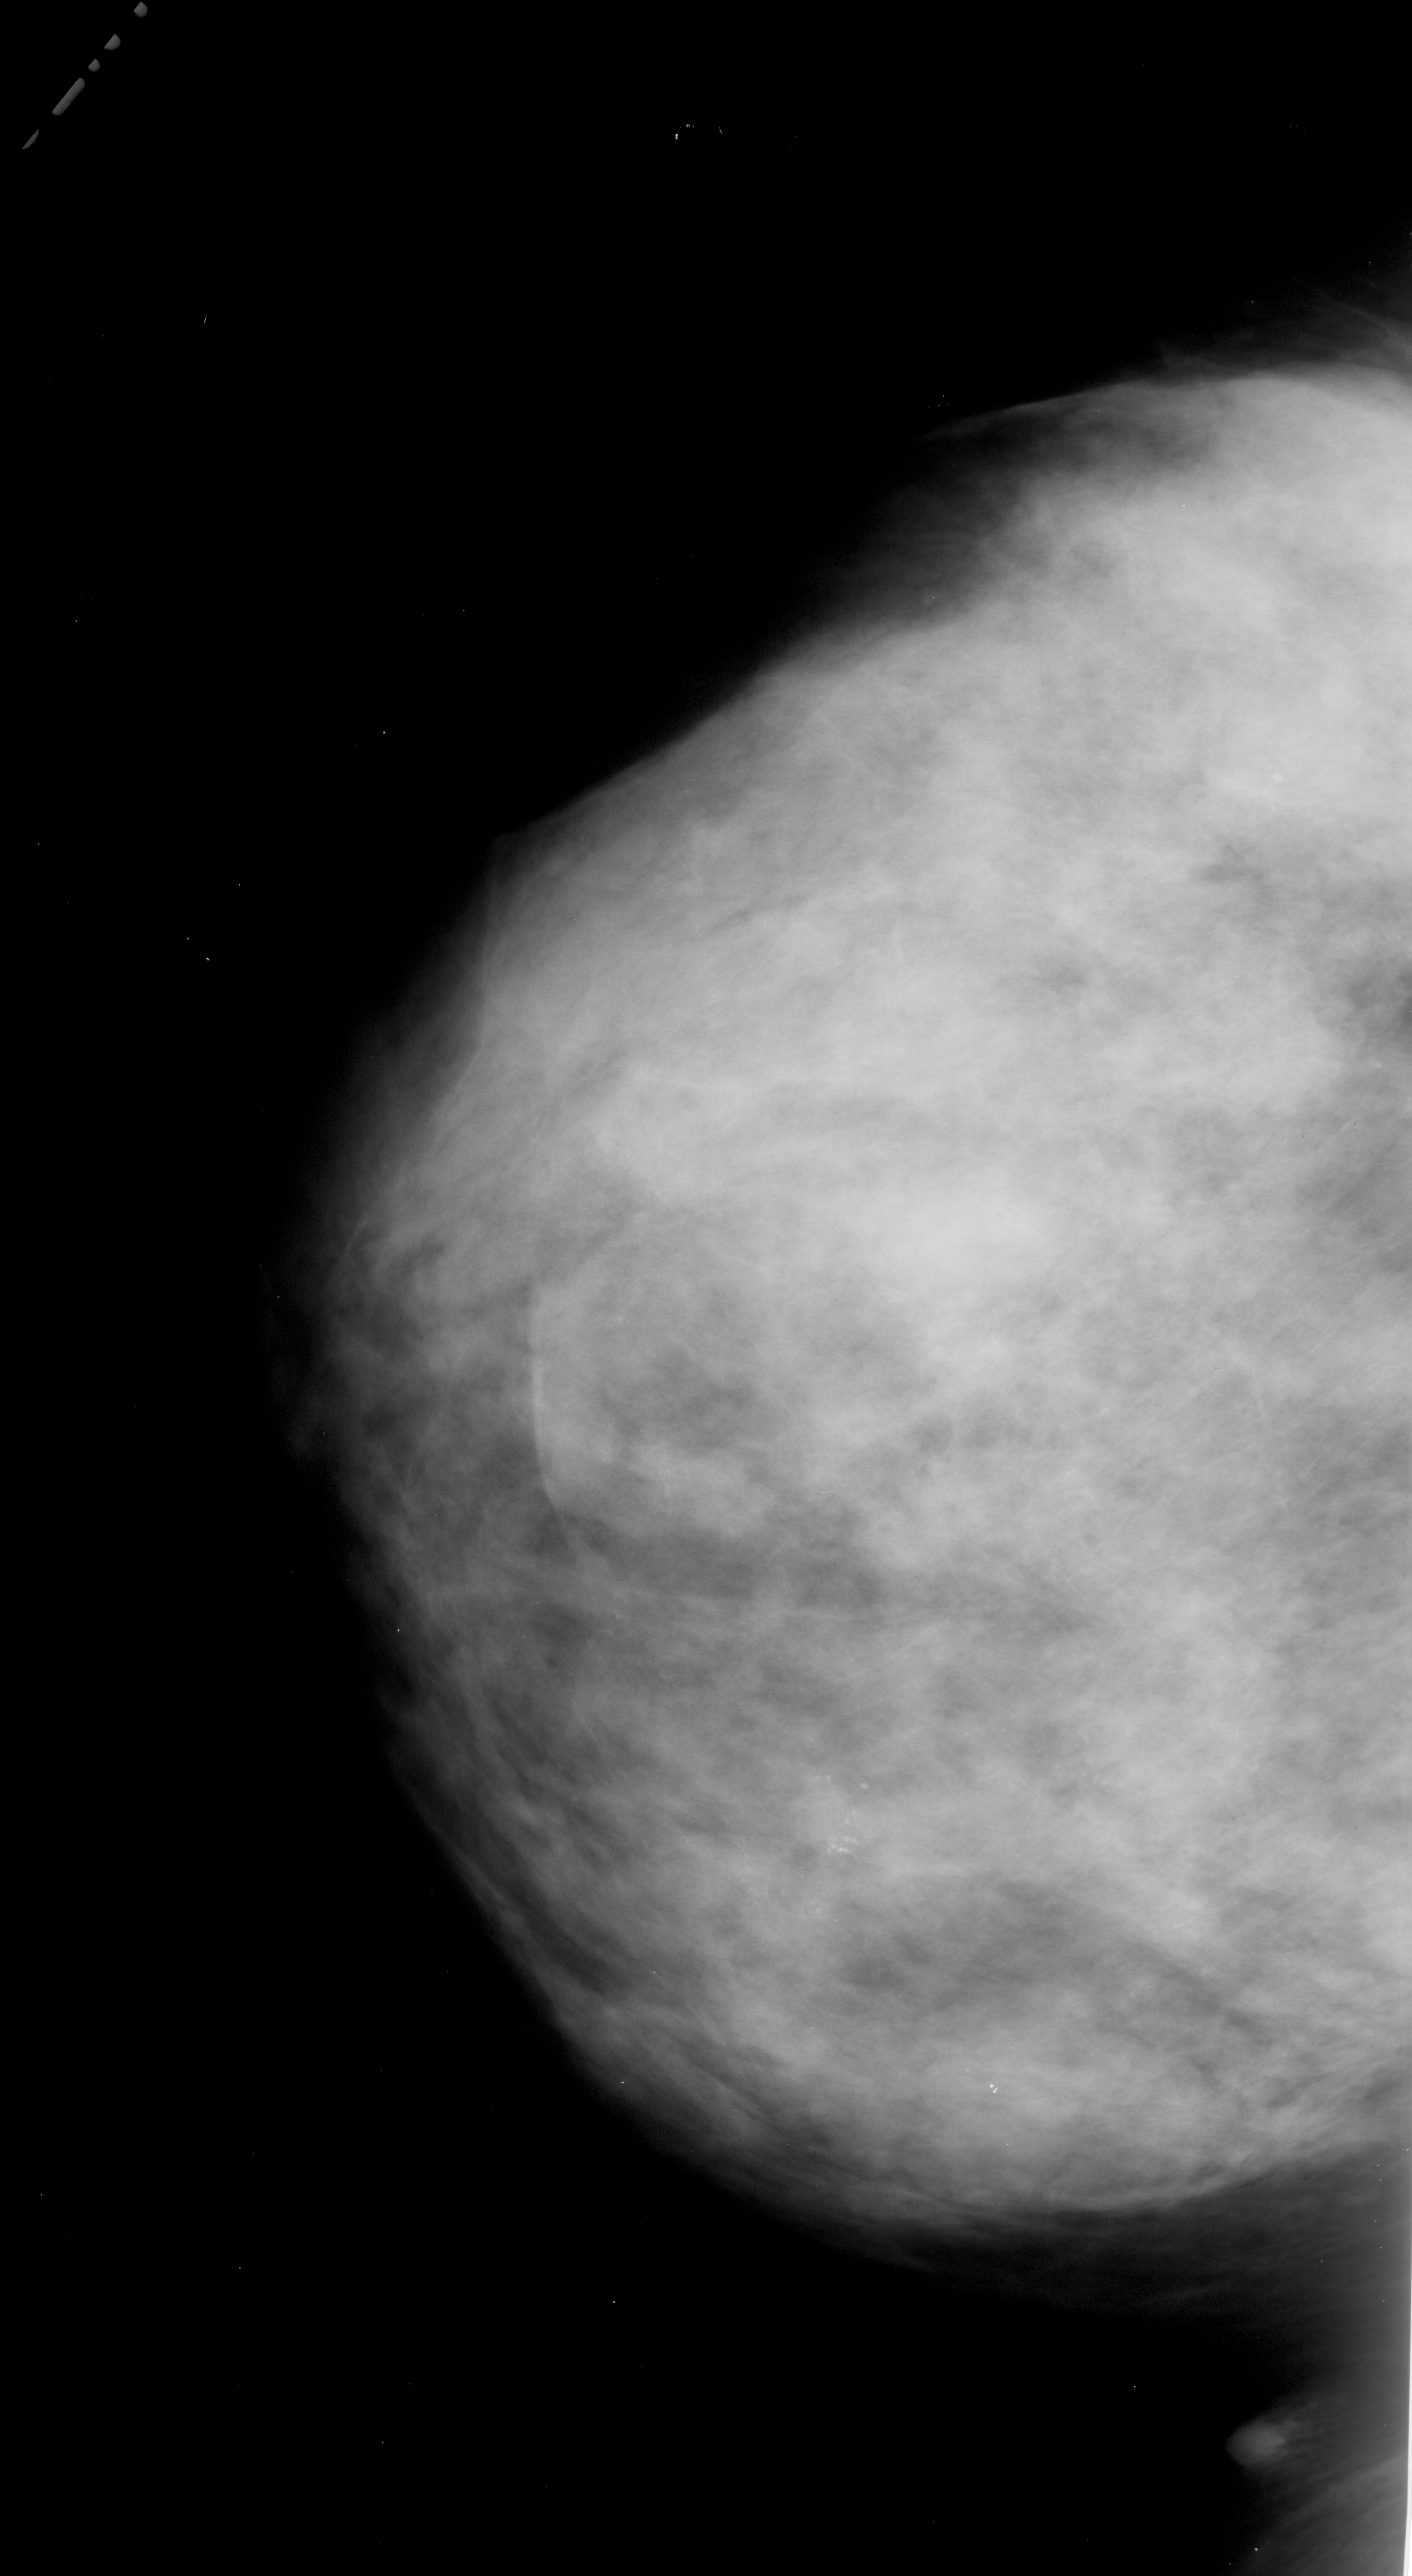
Scanned film-screen mammogram, left breast, craniocaudal (CC) view, breast composition: extremely dense (BI-RADS density category 4 of 4).
Marked abnormality: calcifications, morphology pleomorphic, distribution clustered; BI-RADS assessment category 4; pathology result (as recorded, not read from the image): malignant.